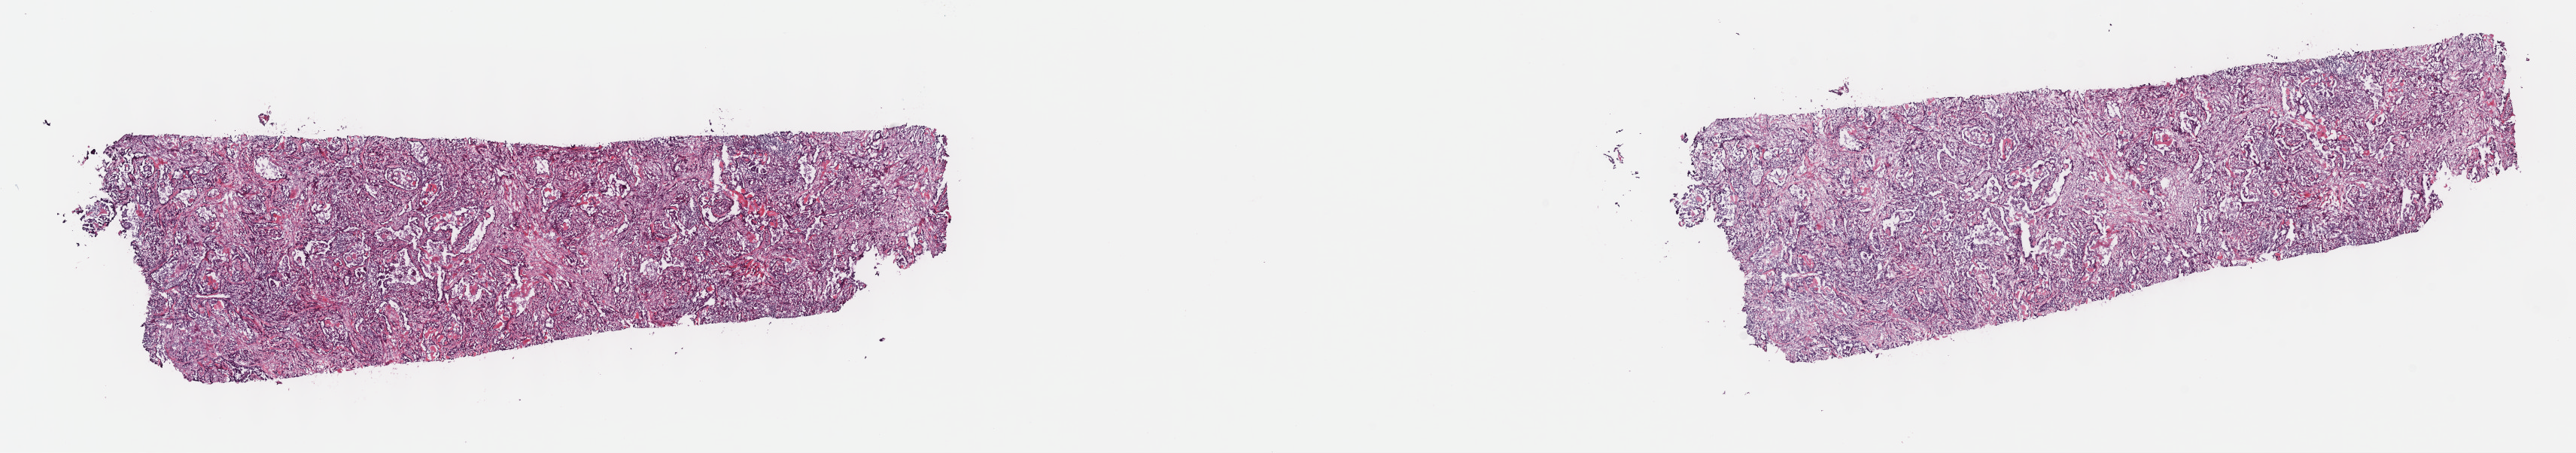
Digitized H&E-stained tissue section (whole slide) — shown as a low-resolution overview of the whole scanned area (about 27.7 x 4.9 mm, from a 40x scan), frozen section from the top of the tissue portion, primary tumour sample from the mesothelium. Male, age 42 years at initial diagnosis. Composition of this section per pathologist review: tumour cells 70%, tumour nuclei 80%, normal cells 0%, stromal cells 30%, necrosis 0%. Infiltration values recorded for this section: lymphocyte infiltration 0%, monocyte infiltration 0%, neutrophil infiltration 0%.
- histologic diagnosis: Epithelioid mesothelioma, malignant (pleura, NOS)
- AJCC pathologic stage: III
- TNM: T3 N0 MX